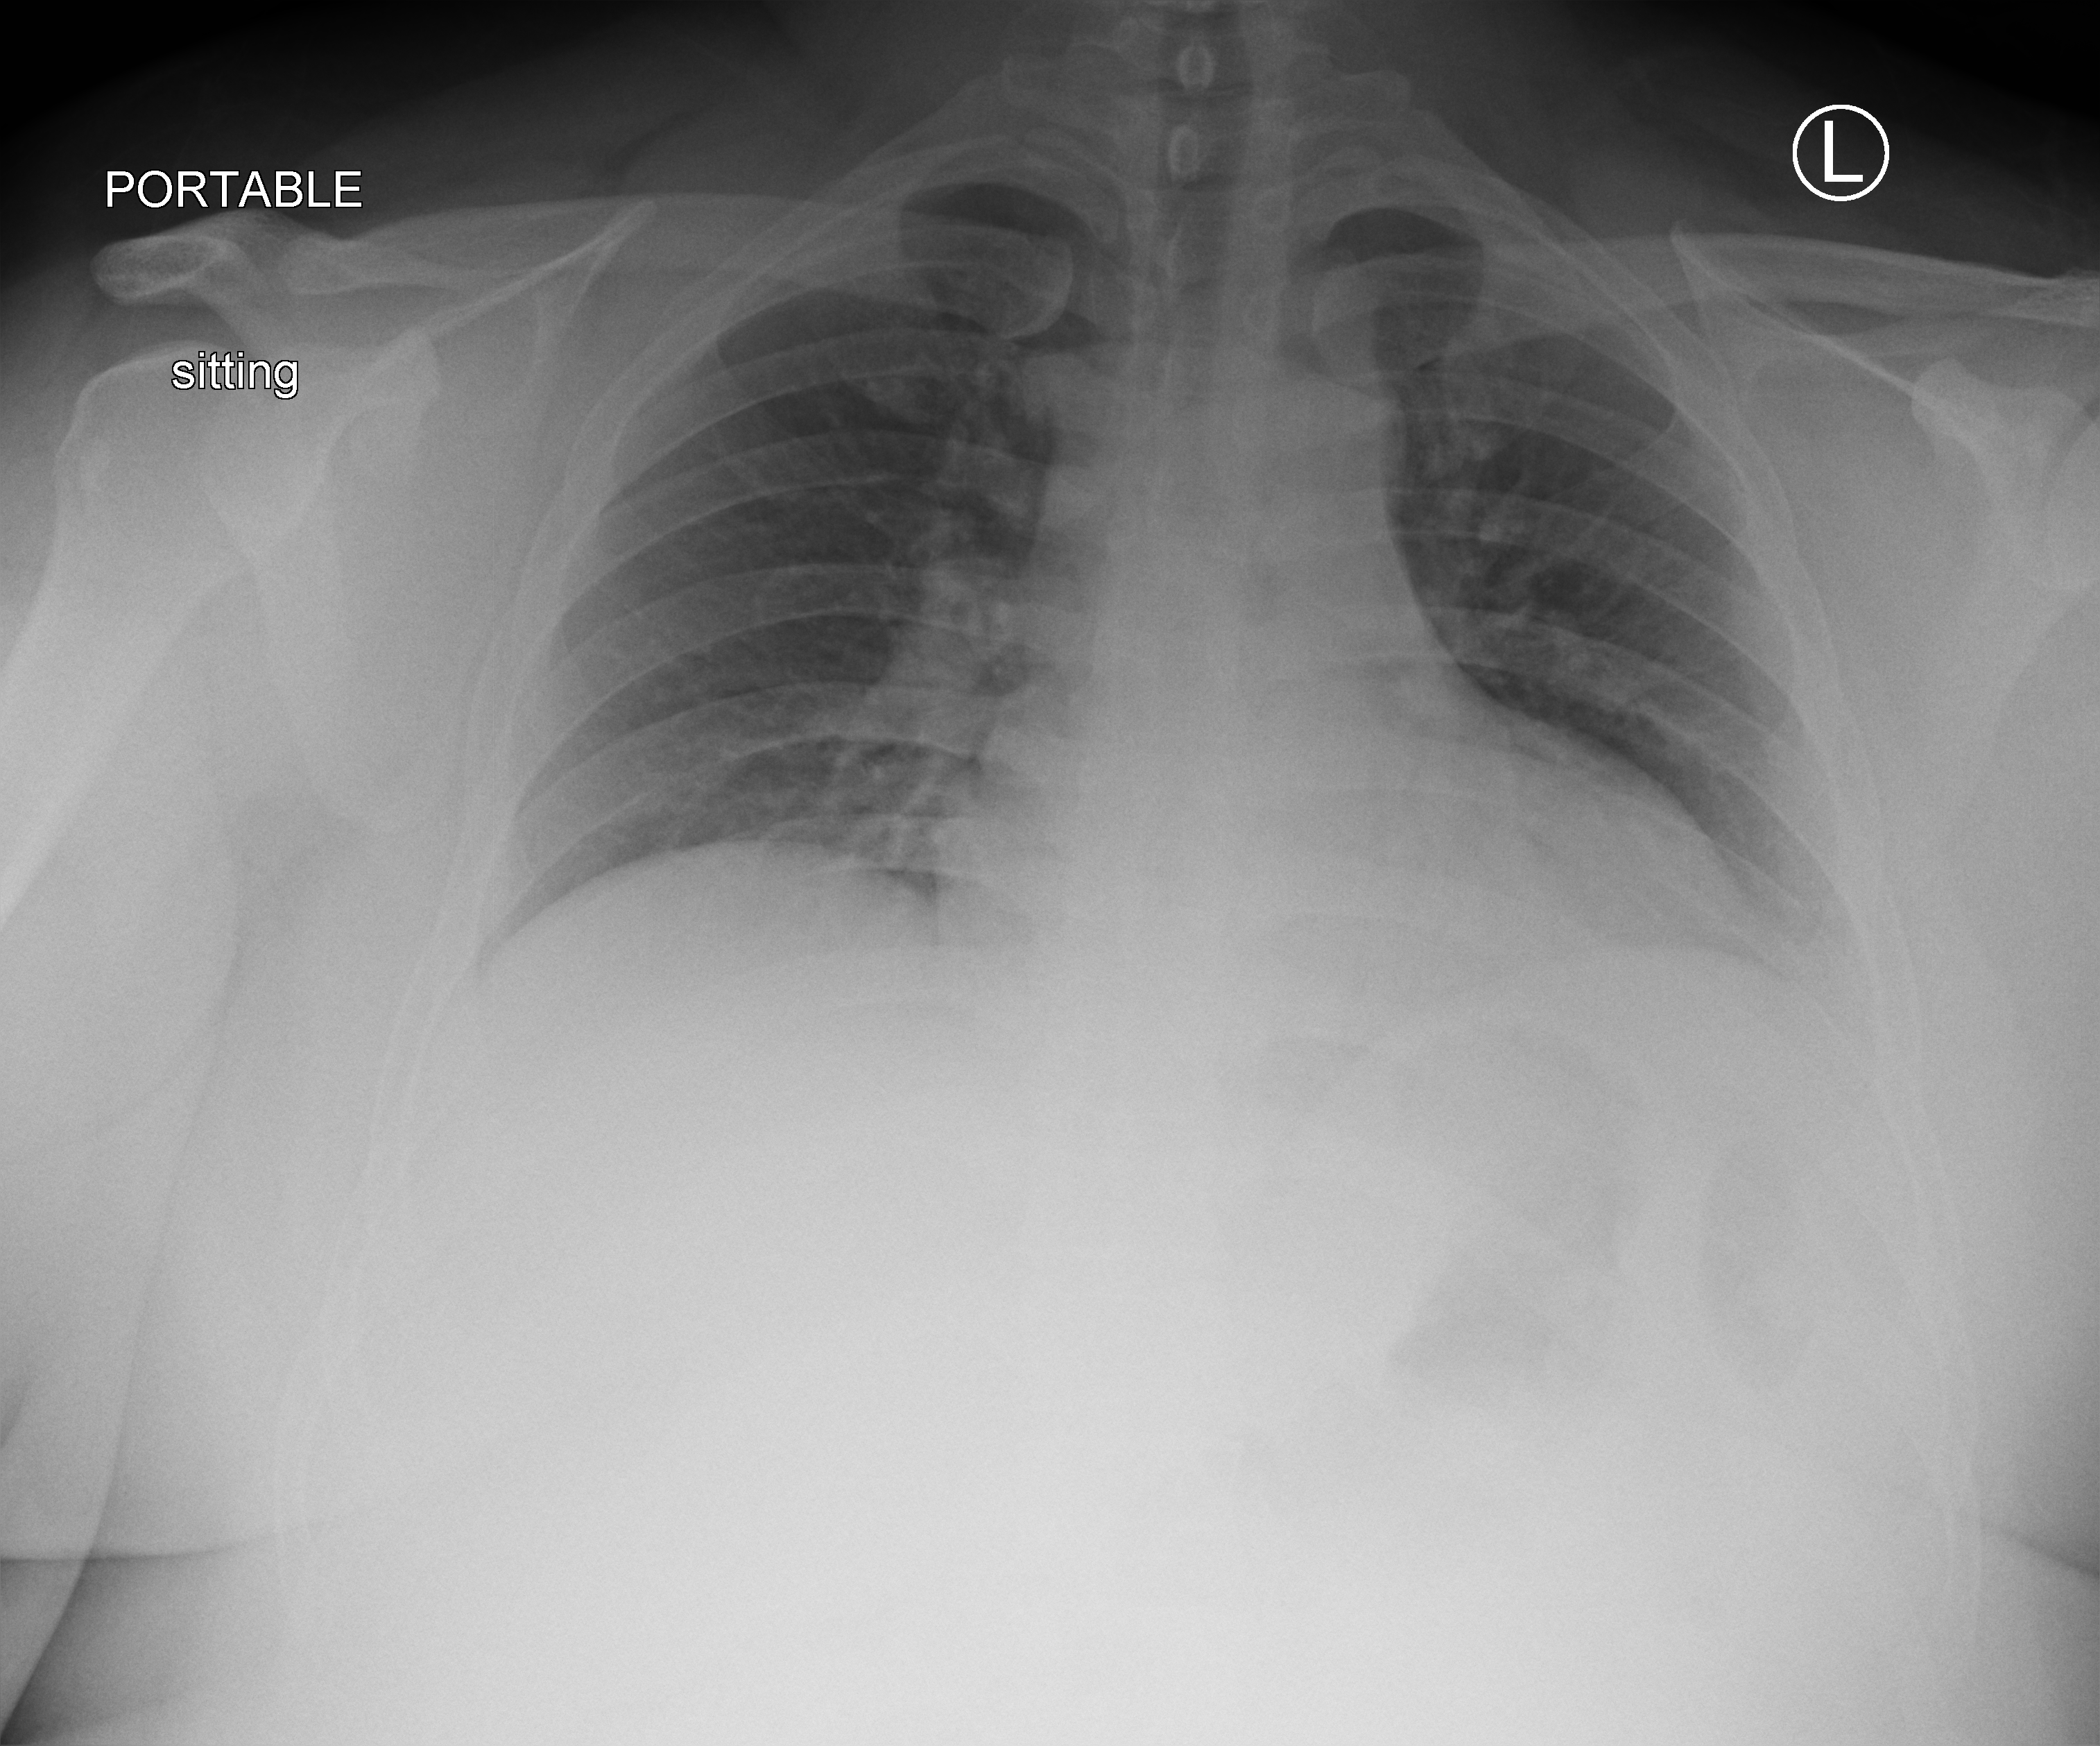
Bedside chest radiograph (computed radiography); anteroposterior (AP) projection. Patient hospitalised with COVID-19; male, aged 18–59 years.
Hospital-stay facts (about this admission, not read from this image; timing relative to this image not recorded):
- admitted to intensive care during this hospital stay: no